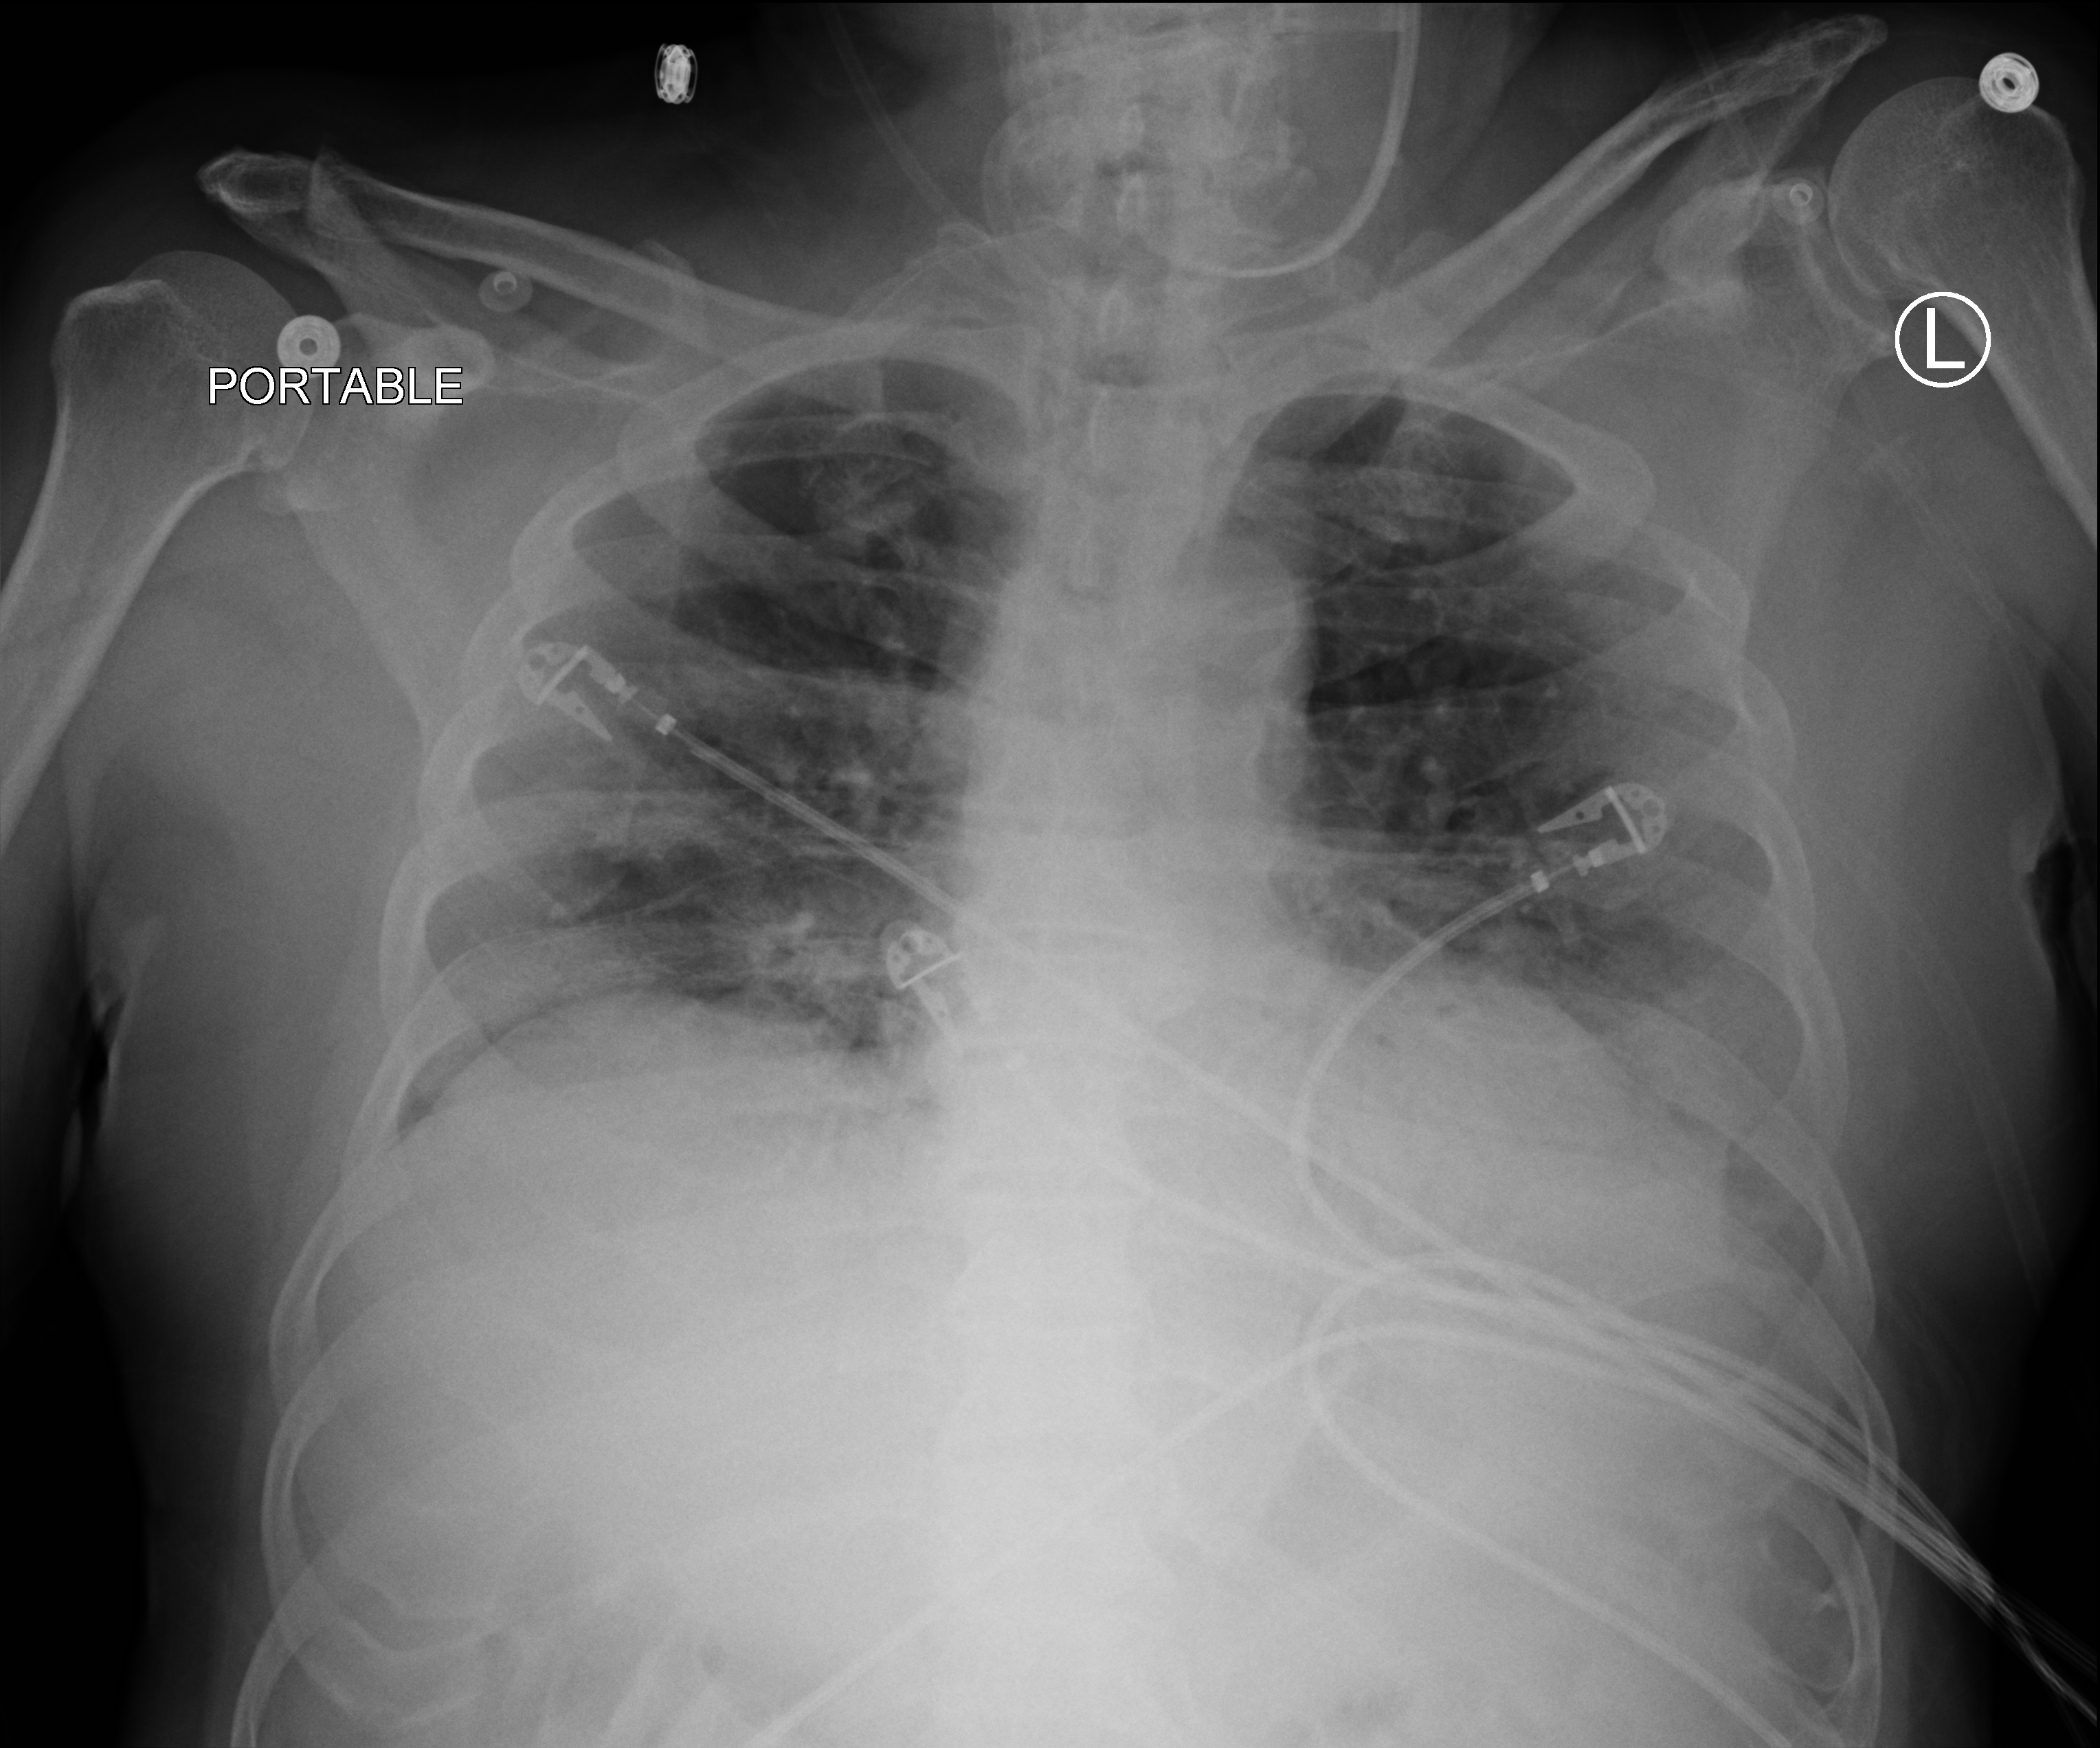
Bedside chest radiograph (computed radiography), anteroposterior (AP) projection. Patient hospitalised with COVID-19; male, aged 75–90 years.
Admission-level facts for this patient (not findings on this image; timing relative to this image not recorded): hypertension (admission record): yes.